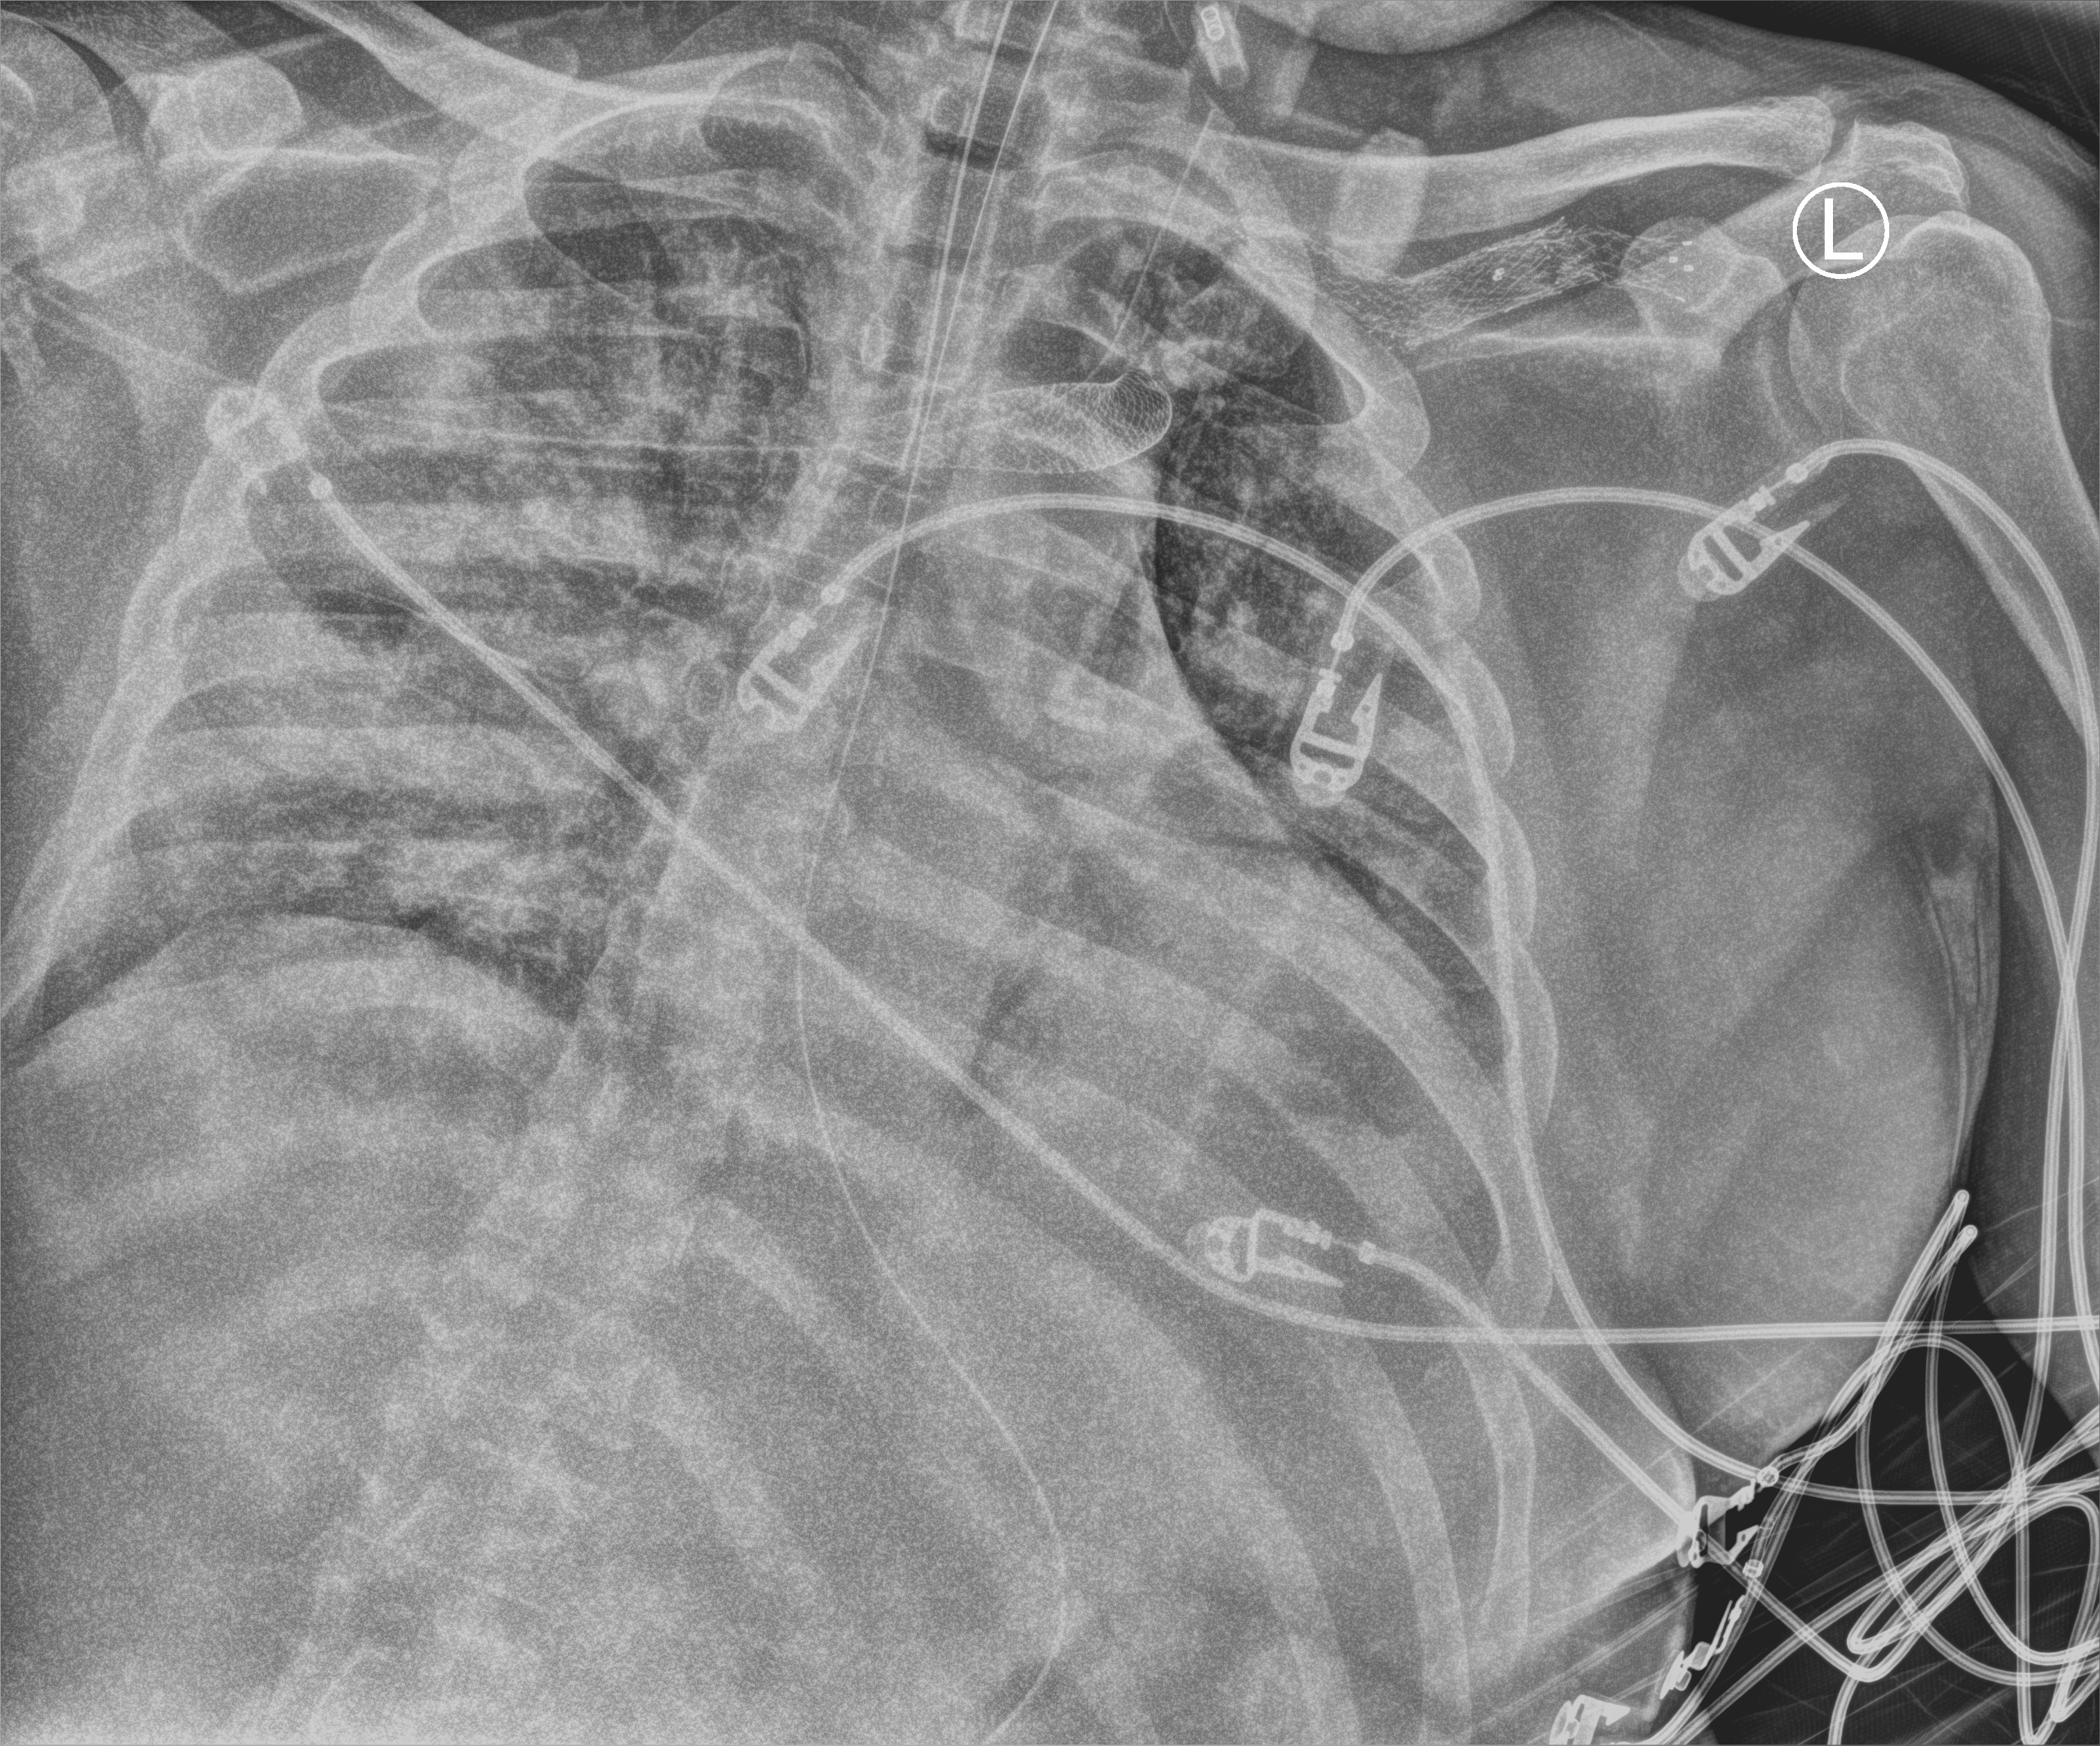
Portable chest radiograph; anteroposterior (AP) projection. Male patient hospitalised with COVID-19, age 18–59 years.
Admission-level facts for this patient (not findings on this image; timing relative to this image not recorded): admitted to intensive care during this hospital stay: yes; chronic kidney disease (admission record): yes.